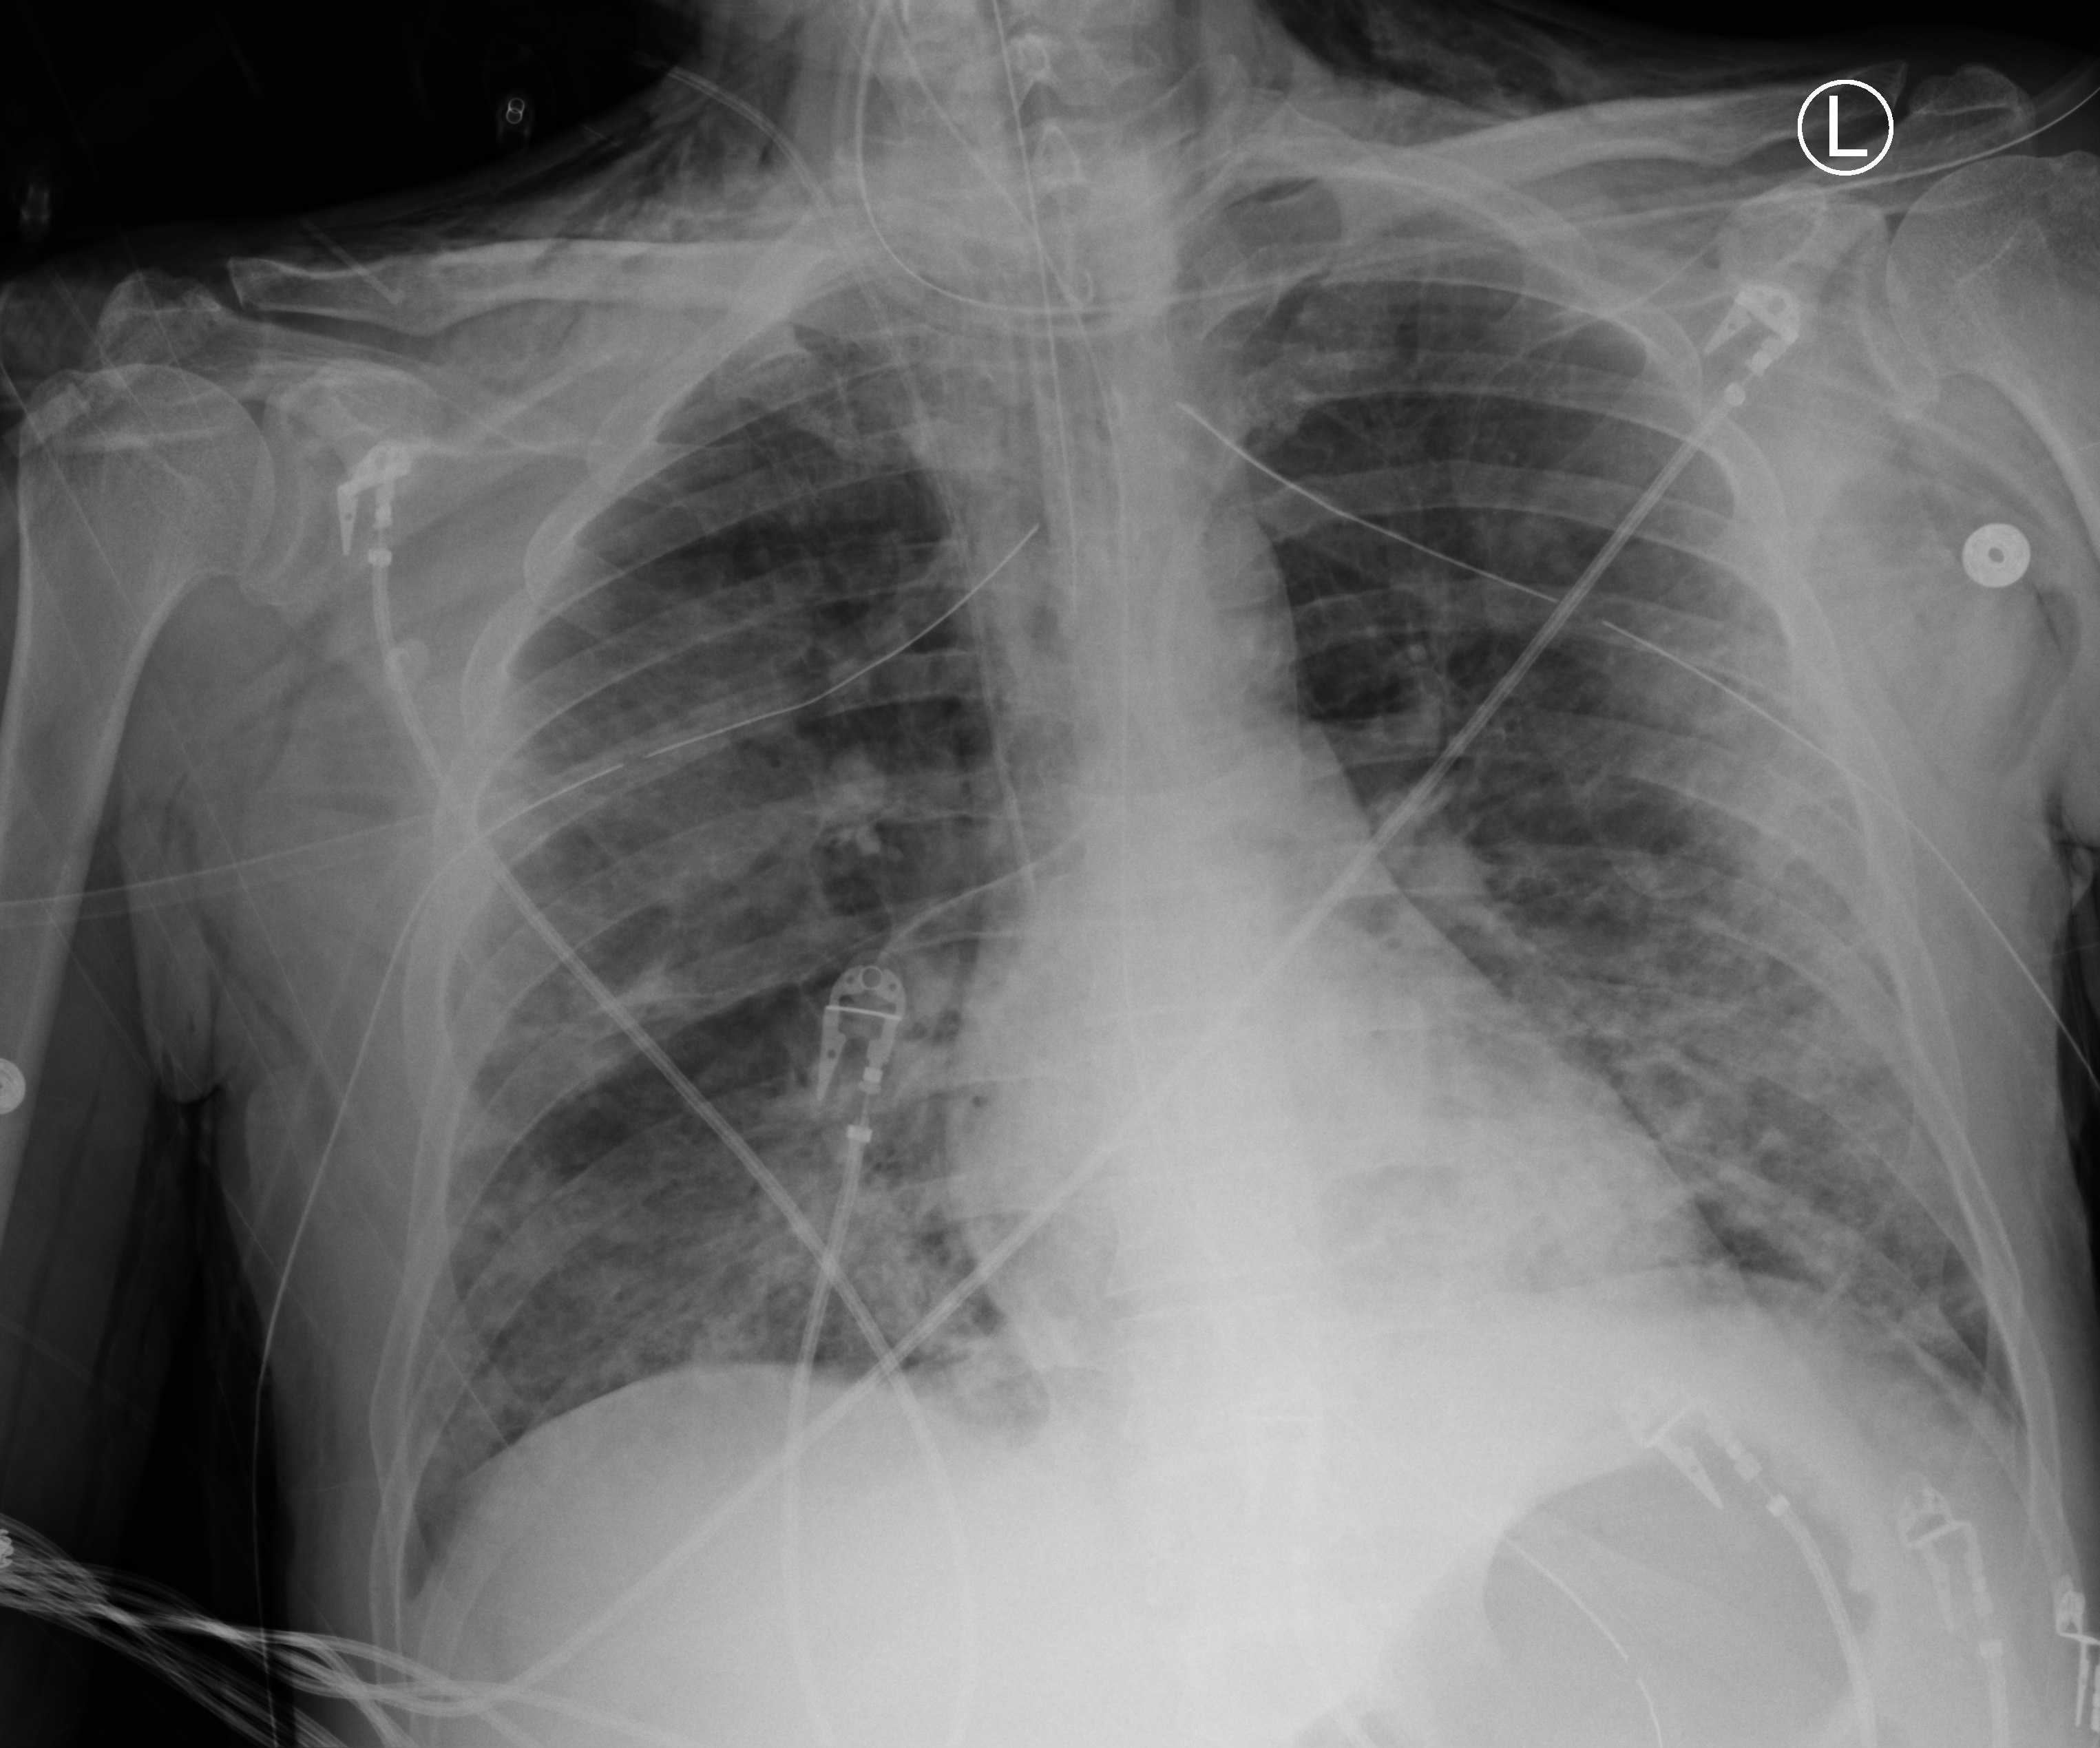
Chest X-ray (portable). Patient hospitalised with COVID-19; male, aged 18–59 years.
From the hospital-stay record, not from the radiograph (when in the stay this image was taken is not recorded): mechanically ventilated during this hospital stay: yes.